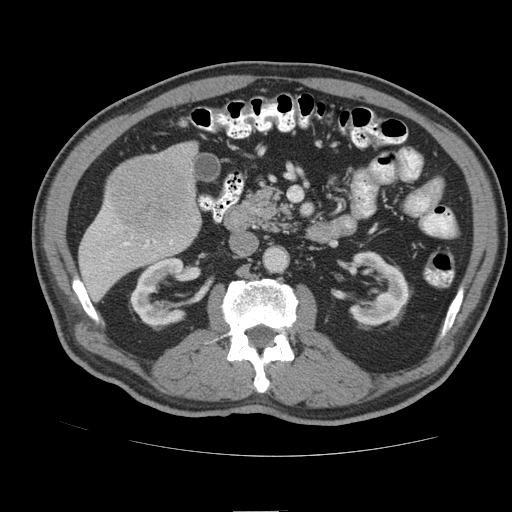
Contrast-enhanced abdominal CT (liver protocol), one axial slice; slice 33 of 105 in the series (ordered by position); soft-tissue window (W 400 / L 40 HU); 2.5 mm slice thickness; 512 × 512 image matrix. Case-level facts recorded for this patient, not image findings: diagnosis: hepatocellular carcinoma (patient treated with transarterial chemoembolisation; whether this scan precedes or follows treatment is not stated here); TNM stage (as recorded): Stage-IIIB.
Annotated regions visible in this slice (semi-automatic segmentation, software-assisted and operator-edited):
- liver parenchyma outside the tumour (the mass and vessels are separate outlines, so this box may not span the whole liver): bounding box (x1, y1, x2, y2) in pixels: (78, 142, 200, 300)
- mass: (109, 157, 191, 236)
- liver vessels: (107, 223, 172, 247)